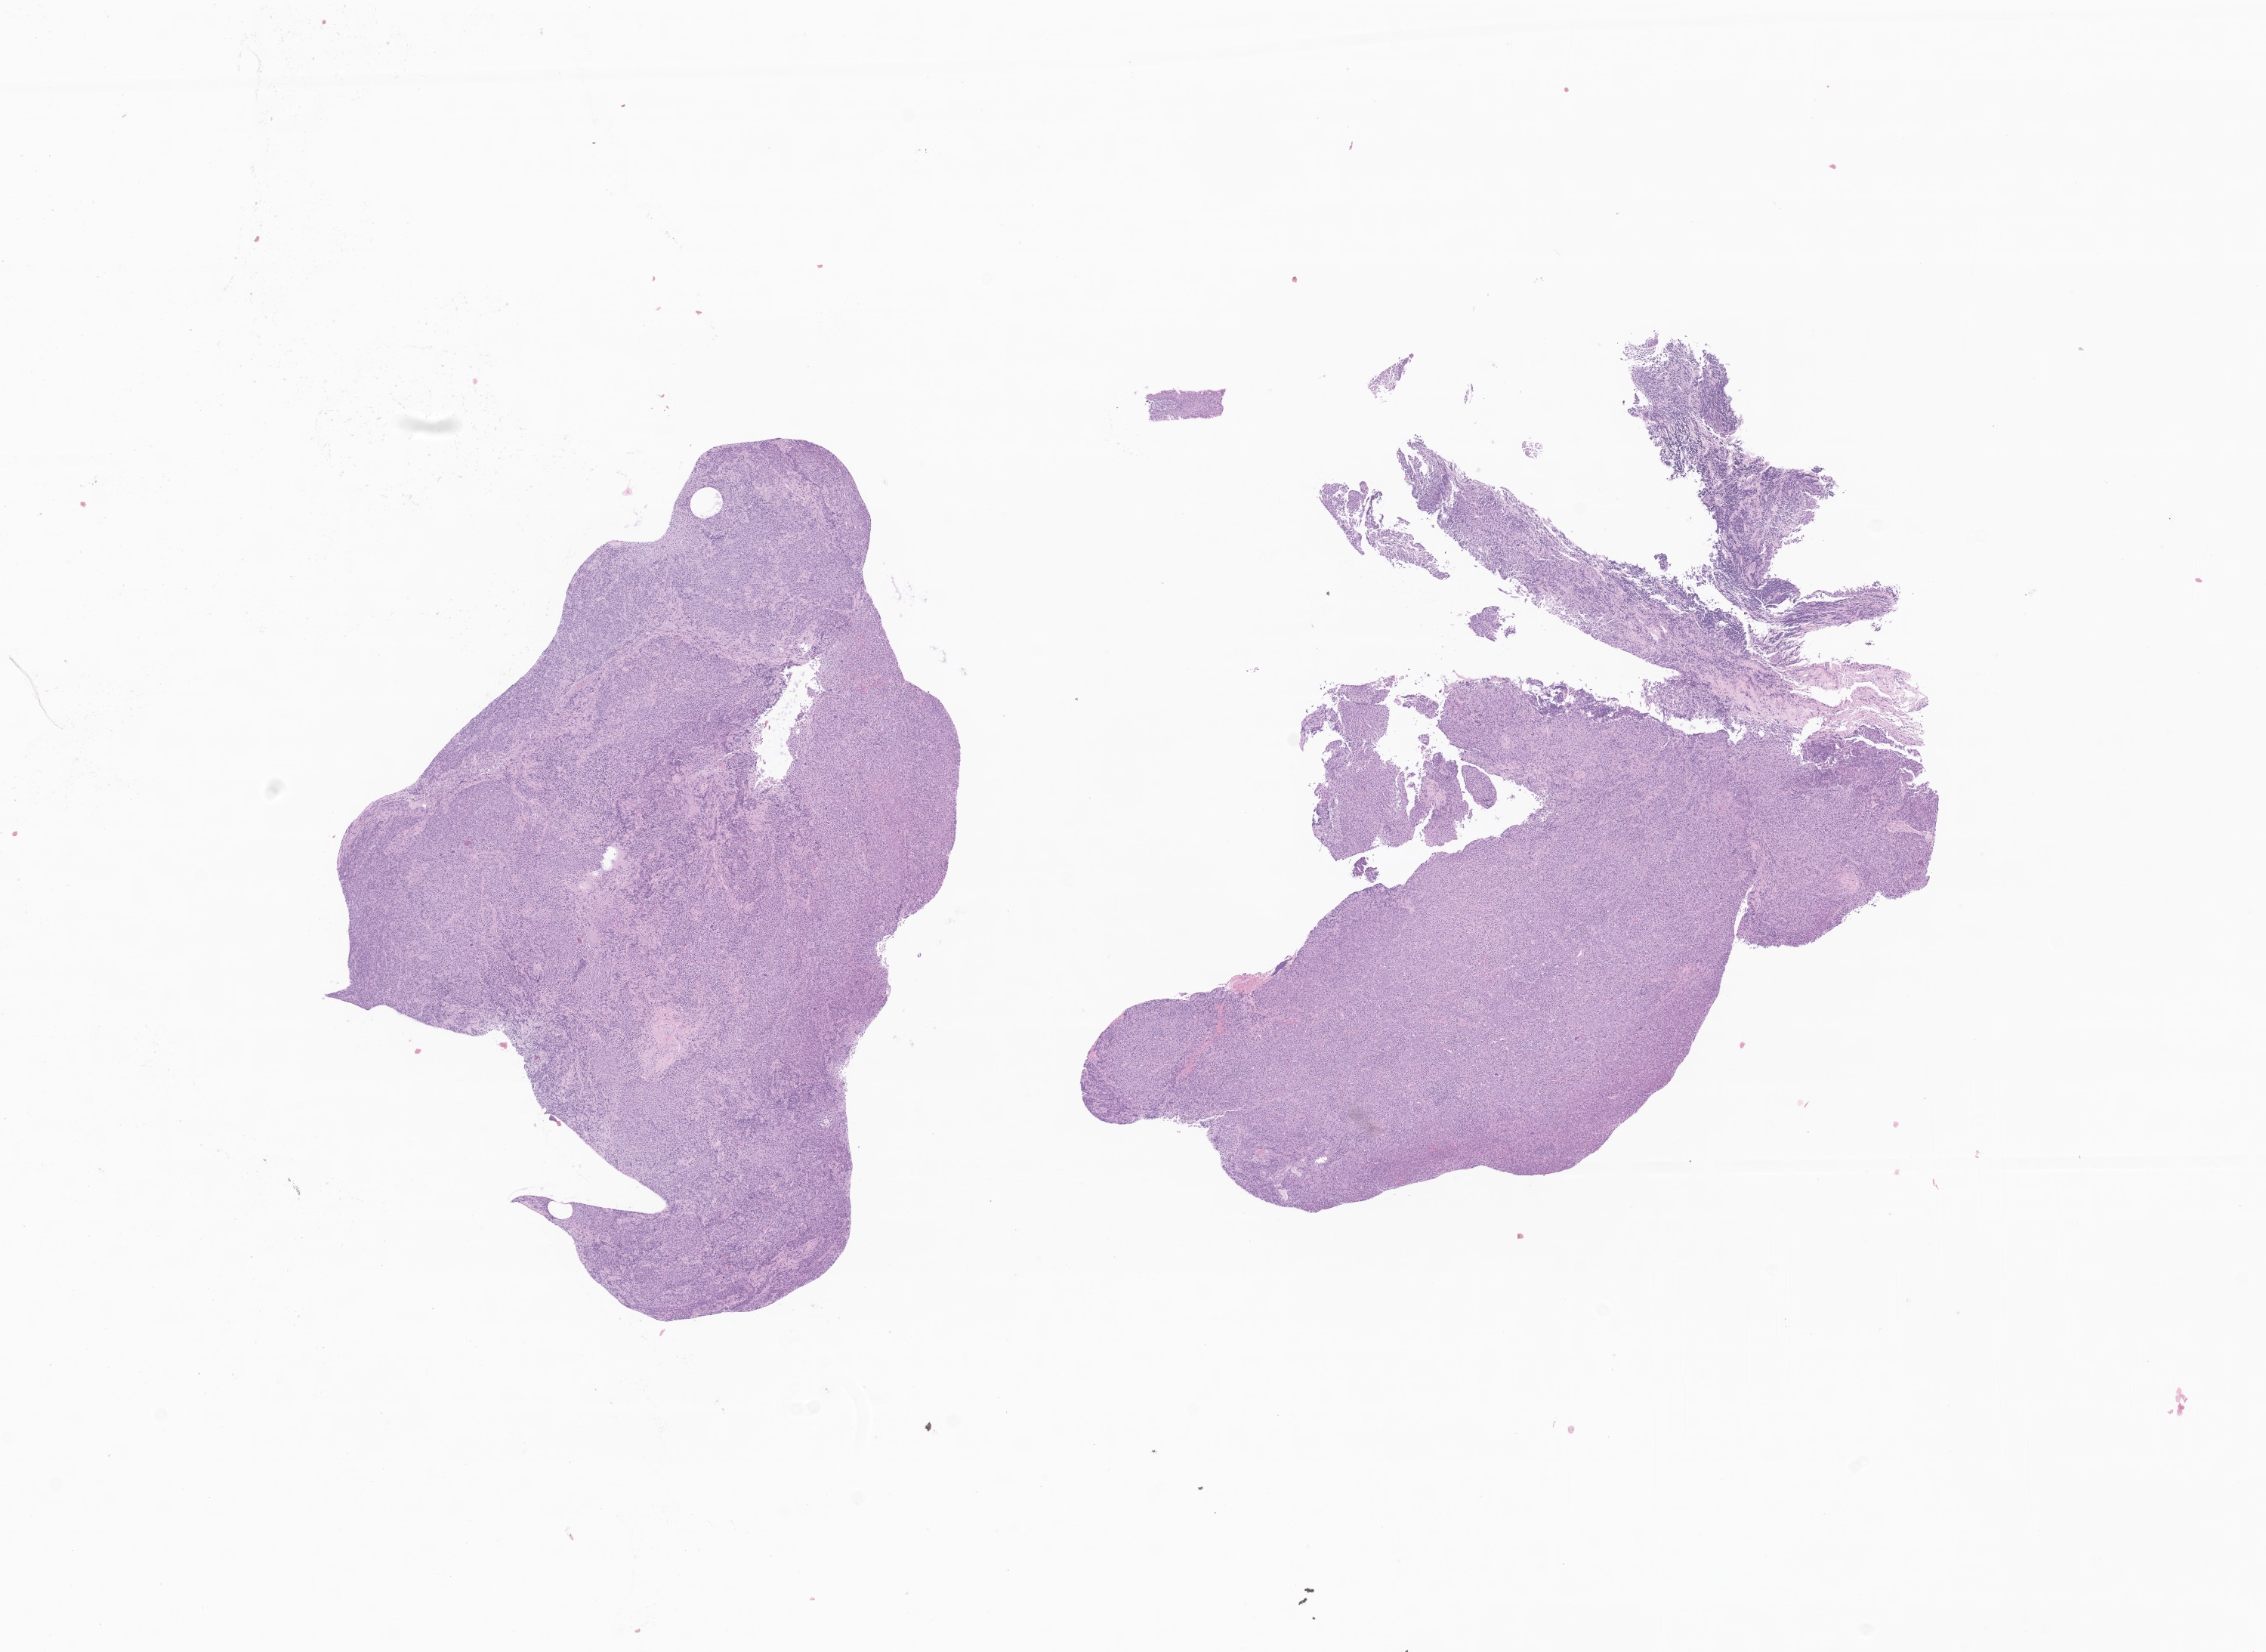
Whole-slide image, H&E stain of tumor tissue from the nasopharynx, shown as a low-resolution overview of the whole scanned area (about 12.6 x 9.2 mm). Formalin-fixed, paraffin-embedded (FFPE) tissue. Patient male; age 173 months.
Recorded diagnosis: Squamous cell carcinoma, small cell, nonkeratinizing.